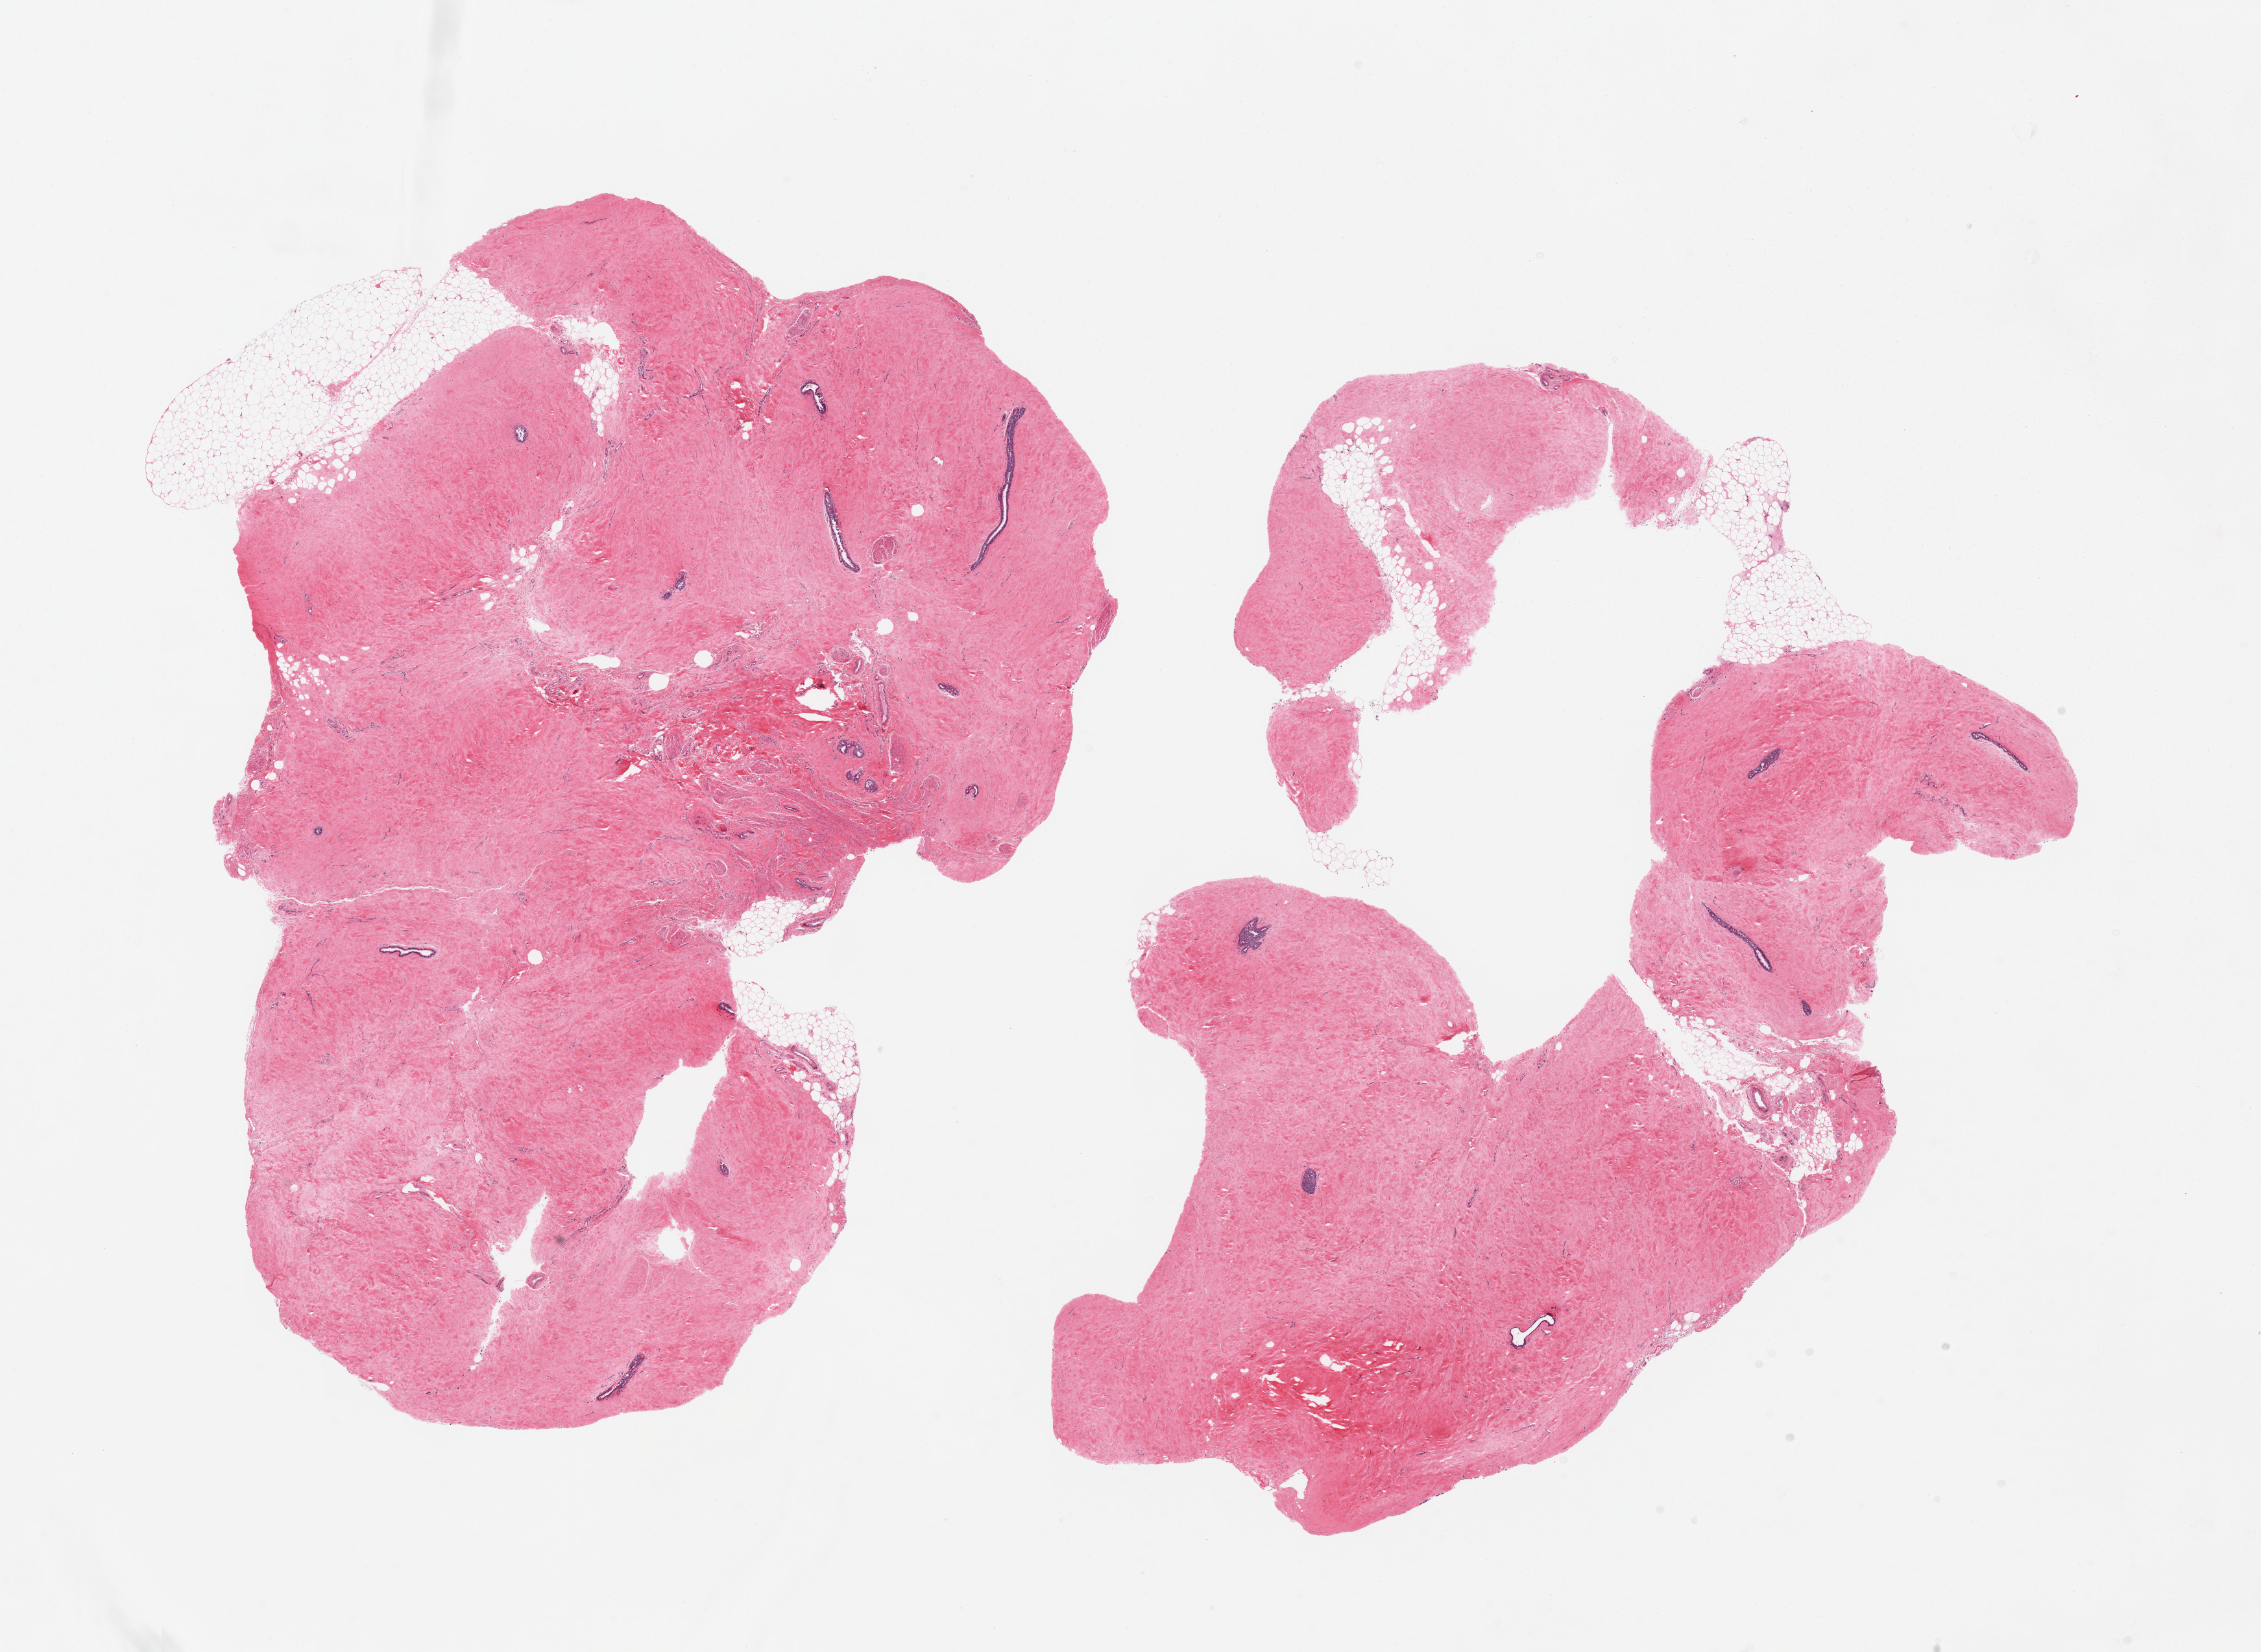
H&E whole-slide image, brightfield, whole scanned area (about 27.6 x 20.1 mm) shown as a low-resolution overview, PAXgene-fixed paraffin-embedded (PFPE) section, target tissue: breast, donor tissue sample. Donor: male.
Reviewer comment on this tissue sample: 2 pieces, gynecomastoid change.